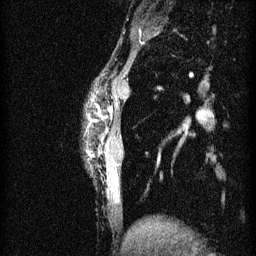
Breast MRI (dynamic contrast-enhanced), one sagittal slice; slice 8 of 60 in the series (ordered by position); 3 images stored at this slice position (order not interpretable as contrast timing); 1.5 T; TE 4.2 ms, TR 11 ms; 2 mm slice thickness; 256 × 256 image matrix, field of view 180 × 180 mm. Female patient, age 40 years.
Annotated regions visible in this slice (semi-automatically segmented with operator editing):
- analysis volume of interest (the breast-tissue region the enhancement analysis was run in; not a lesion): bounding box <88,82,130,187> (left, top, right, bottom; pixels)
- tumour enhancement mask (voxels above the 70 % enhancement threshold inside the analysis volume of interest): <110,108,115,177>